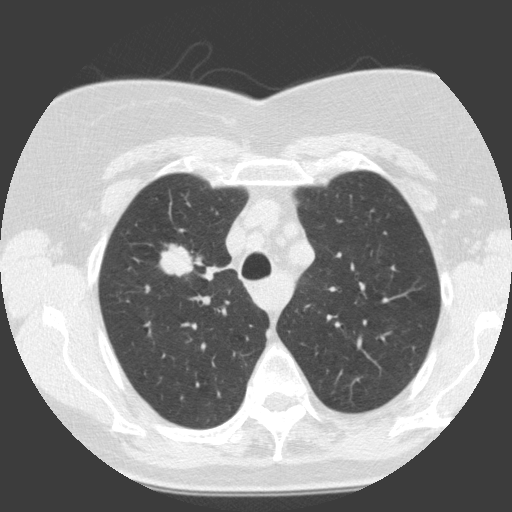
Low-dose screening chest CT, axial slice. Baseline screening round. Lung window (W 1500 / L -600 HU). 2 mm slice thickness. Standard (soft-tissue) reconstruction kernel (C). Slice 36 of 146 in the series. Female, age 68 years at enrolment. Current smoker at enrolment.
Expert reader's lesion annotation, box from (x=155, y=237) to (x=205, y=283) px. Reader record for this screening exam (exam-level; its link to the box is not recorded): non-calcified nodule or mass ≥4 mm, right upper lobe, 19 × 12 mm, smooth margins, soft tissue attenuation. Participant outcome: lung cancer diagnosed 30 days after this screen — squamous cell carcinoma, NOS, right upper lobe, moderately differentiated (G2), stage IA (AJCC 6th edition), 28 mm at pathology.